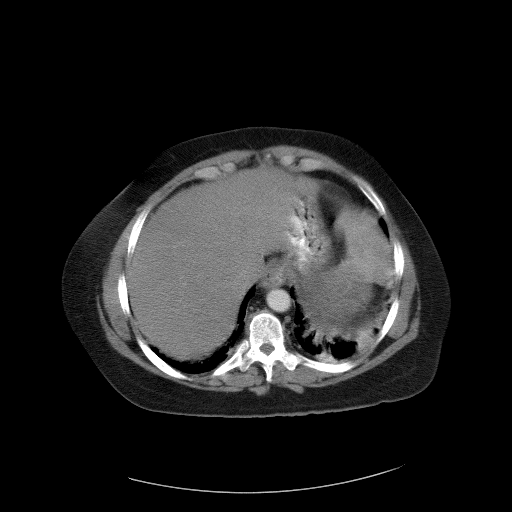
Contrast-enhanced abdominal CT, one axial slice; position 85 of 90 along the scan axis; reconstruction kernel FC01; 120 kVp; intravenous contrast given; soft-tissue window (W 400 / L 40 HU); 5 mm slice thickness; 512 × 512 image matrix. Patient: female, 55 years. Case-level facts recorded for this patient, not image findings: diagnosis: adrenocortical carcinoma; tumour side: left adrenal; tumour size at pathology: 22 cm; Ki-67 index: 10 %; stage (as recorded): 3.
Annotated regions visible in this slice (semi-automatic segmentation, software-assisted and operator-edited):
- mass: box from (x=300, y=271) to (x=371, y=328) px